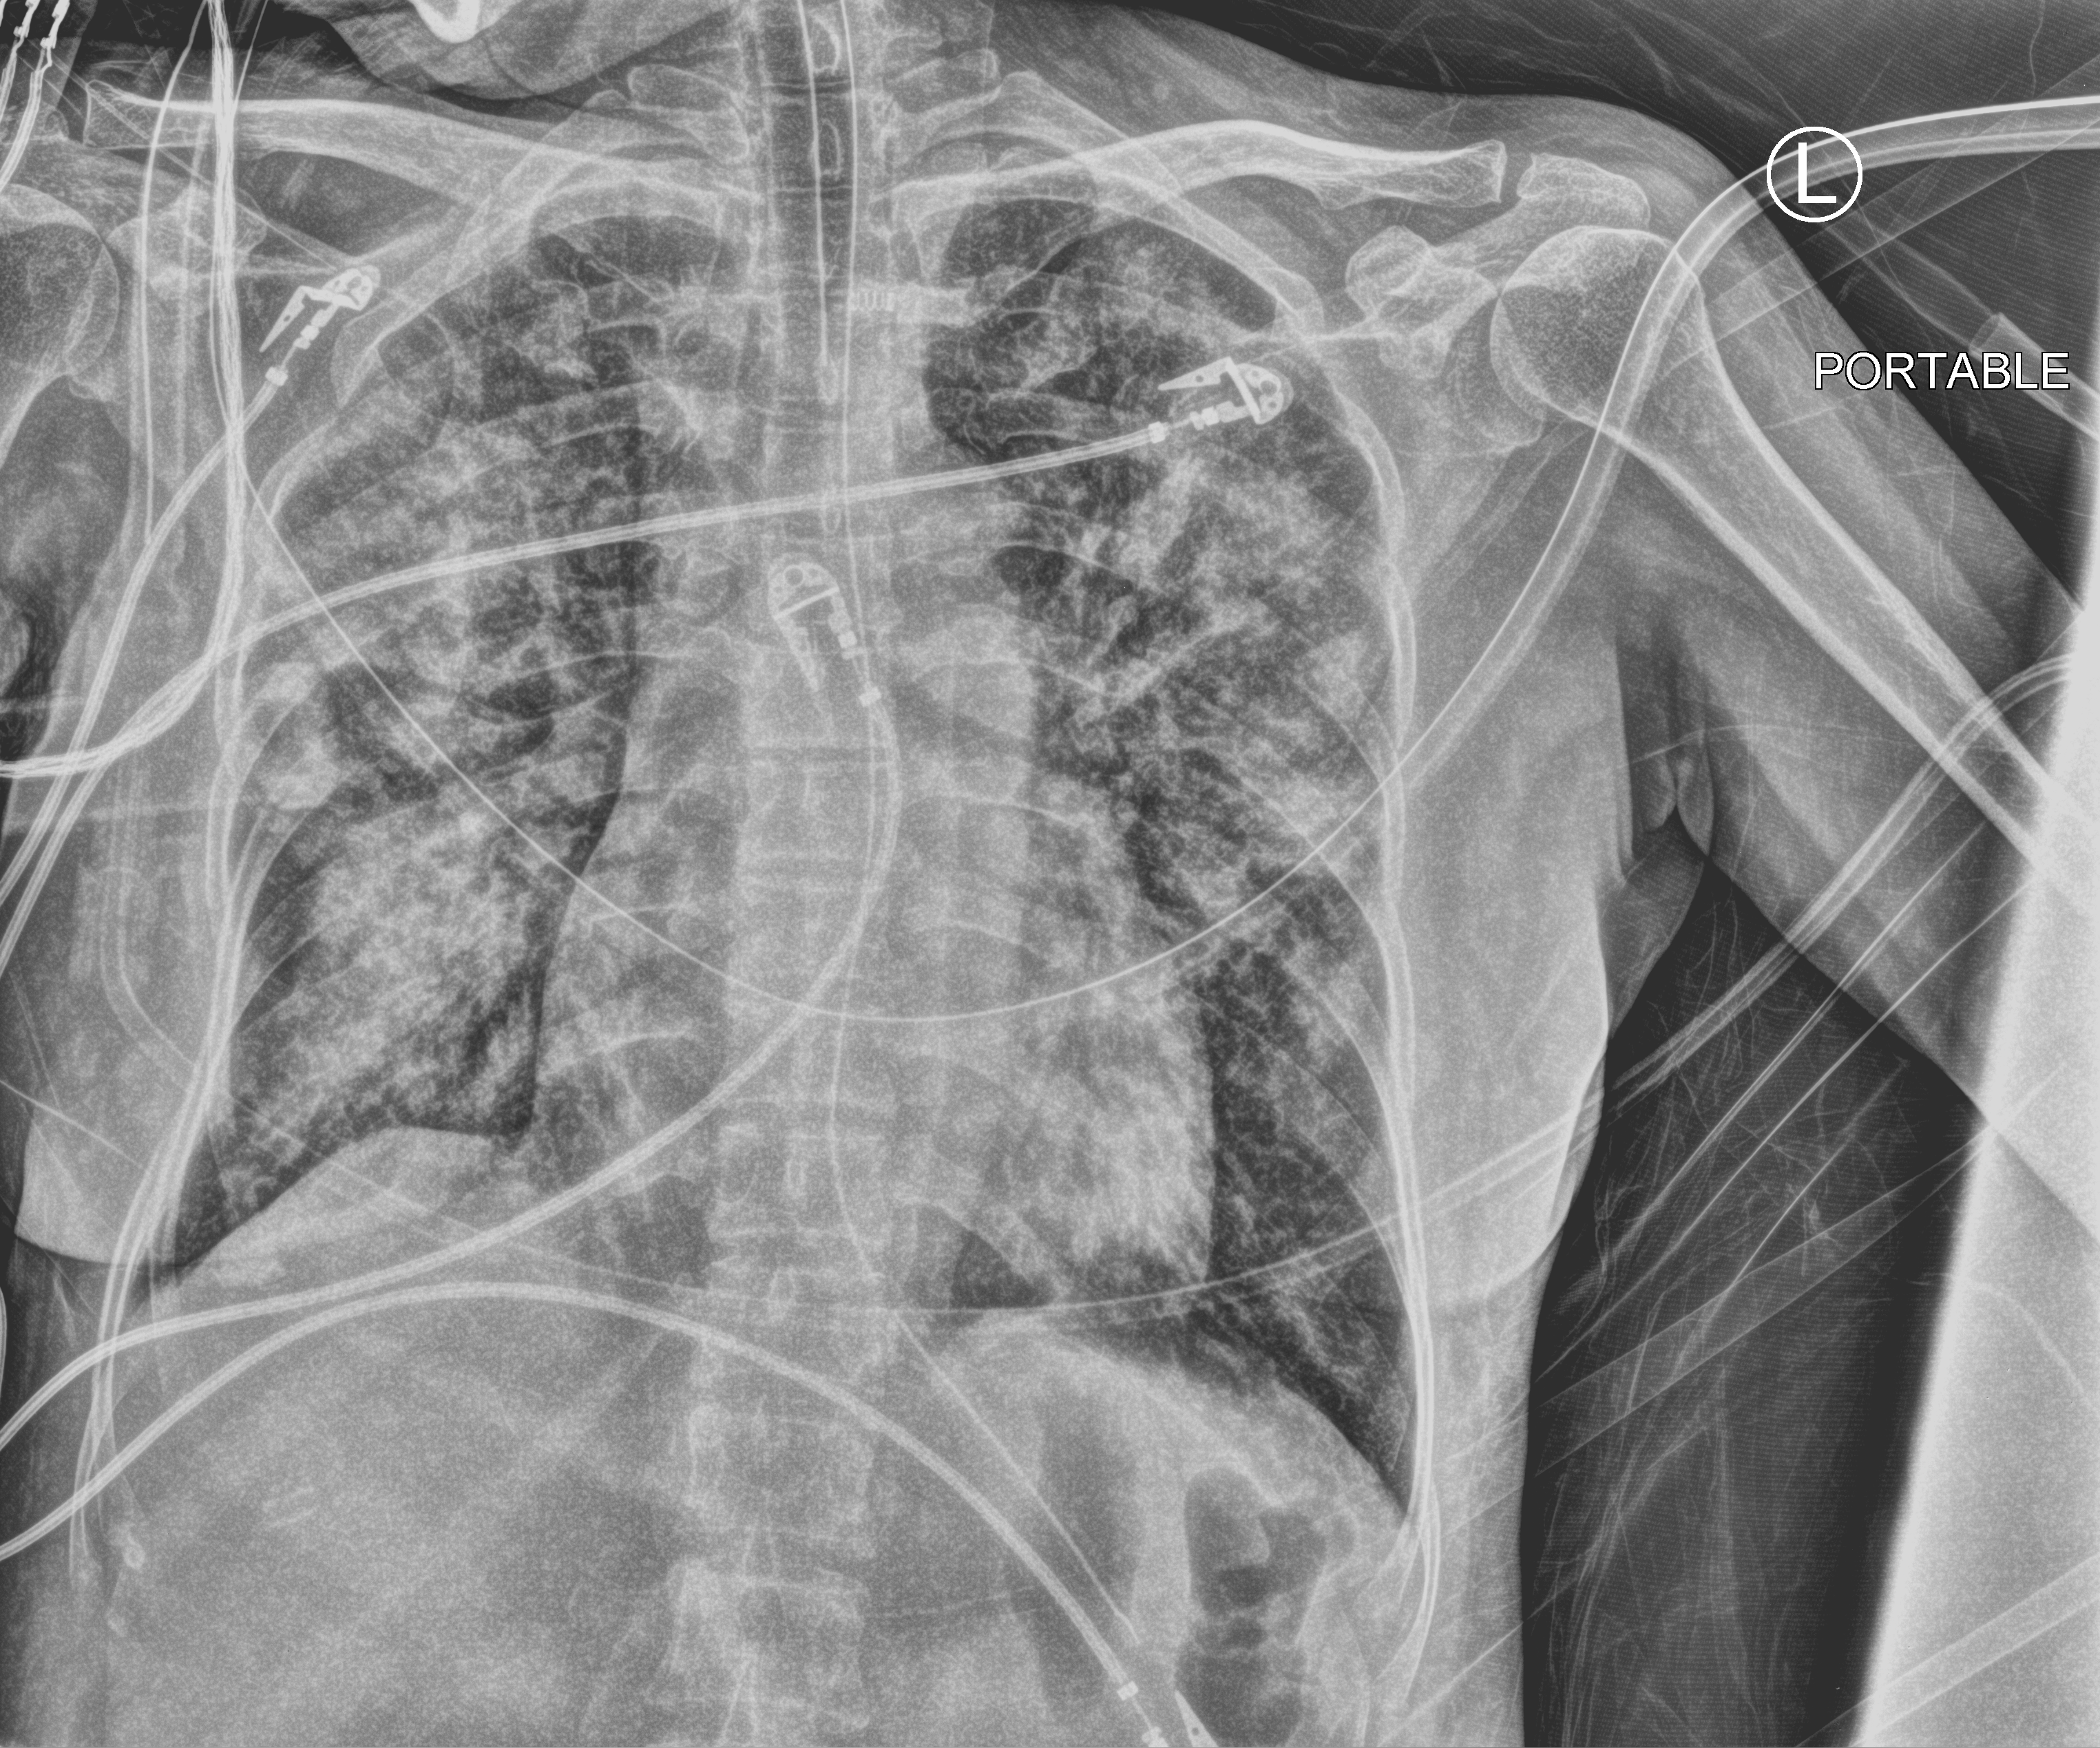
Portable chest radiograph; anteroposterior (AP) projection. Female patient hospitalised with COVID-19, age 60–74 years.
From the hospital-stay record, not from the radiograph (when in the stay this image was taken is not recorded): smoking status (admission record): never.